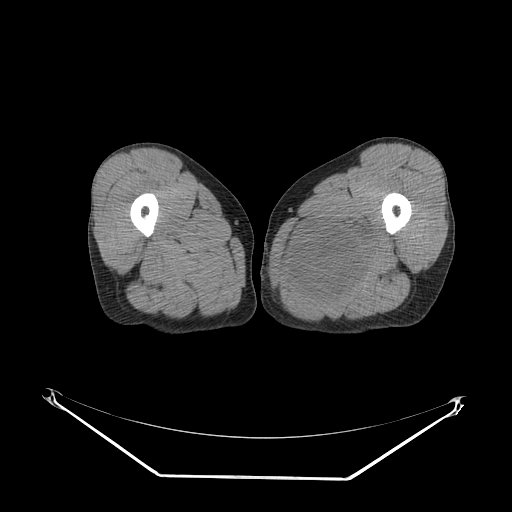
CT of an extremity soft-tissue mass (from a PET/CT study), one axial slice. Slice 22 of 267 in the series (ordered by position). Reconstruction kernel SOFT. 140 kVp. Soft-tissue window (W 400 / L 40 HU). 512 × 512 image matrix, field of view 500 × 500 mm. Male patient. Case-level facts recorded for this patient, not image findings: histological type: pleiomorphic liposarcoma; grade: high; site of the primary tumour: left thigh.
Annotated regions visible in this slice (expert contour drawn on MRI and transferred to this co-registered scan by the dataset authors):
- gross tumour volume including surrounding oedema: bounding box (x1, y1, x2, y2) in pixels: (290, 212, 385, 305)
- gross tumour volume (mass): (294, 219, 369, 300)